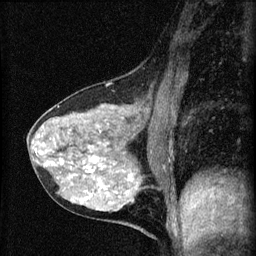
Breast MRI (dynamic contrast-enhanced), one sagittal slice. Position 26 of 60 along the scan axis. Dynamic contrast-enhanced series, image 2 of 4 at this slice position (ordered by acquisition). 1.5 T. TE 4.2 ms, TR 8.2 ms. 2 mm slice thickness. 256 × 256 image matrix, field of view 180 × 180 mm. Female patient, age 41 years.
Annotated regions visible in this slice (semi-automatically segmented with operator editing):
- analysis volume of interest (the breast-tissue region the enhancement analysis was run in; not a lesion): bounding box (x1, y1, x2, y2) in pixels: (28, 91, 166, 210)
- tumour enhancement mask (voxels above the 70 % enhancement threshold inside the analysis volume of interest): (34, 129, 132, 202)